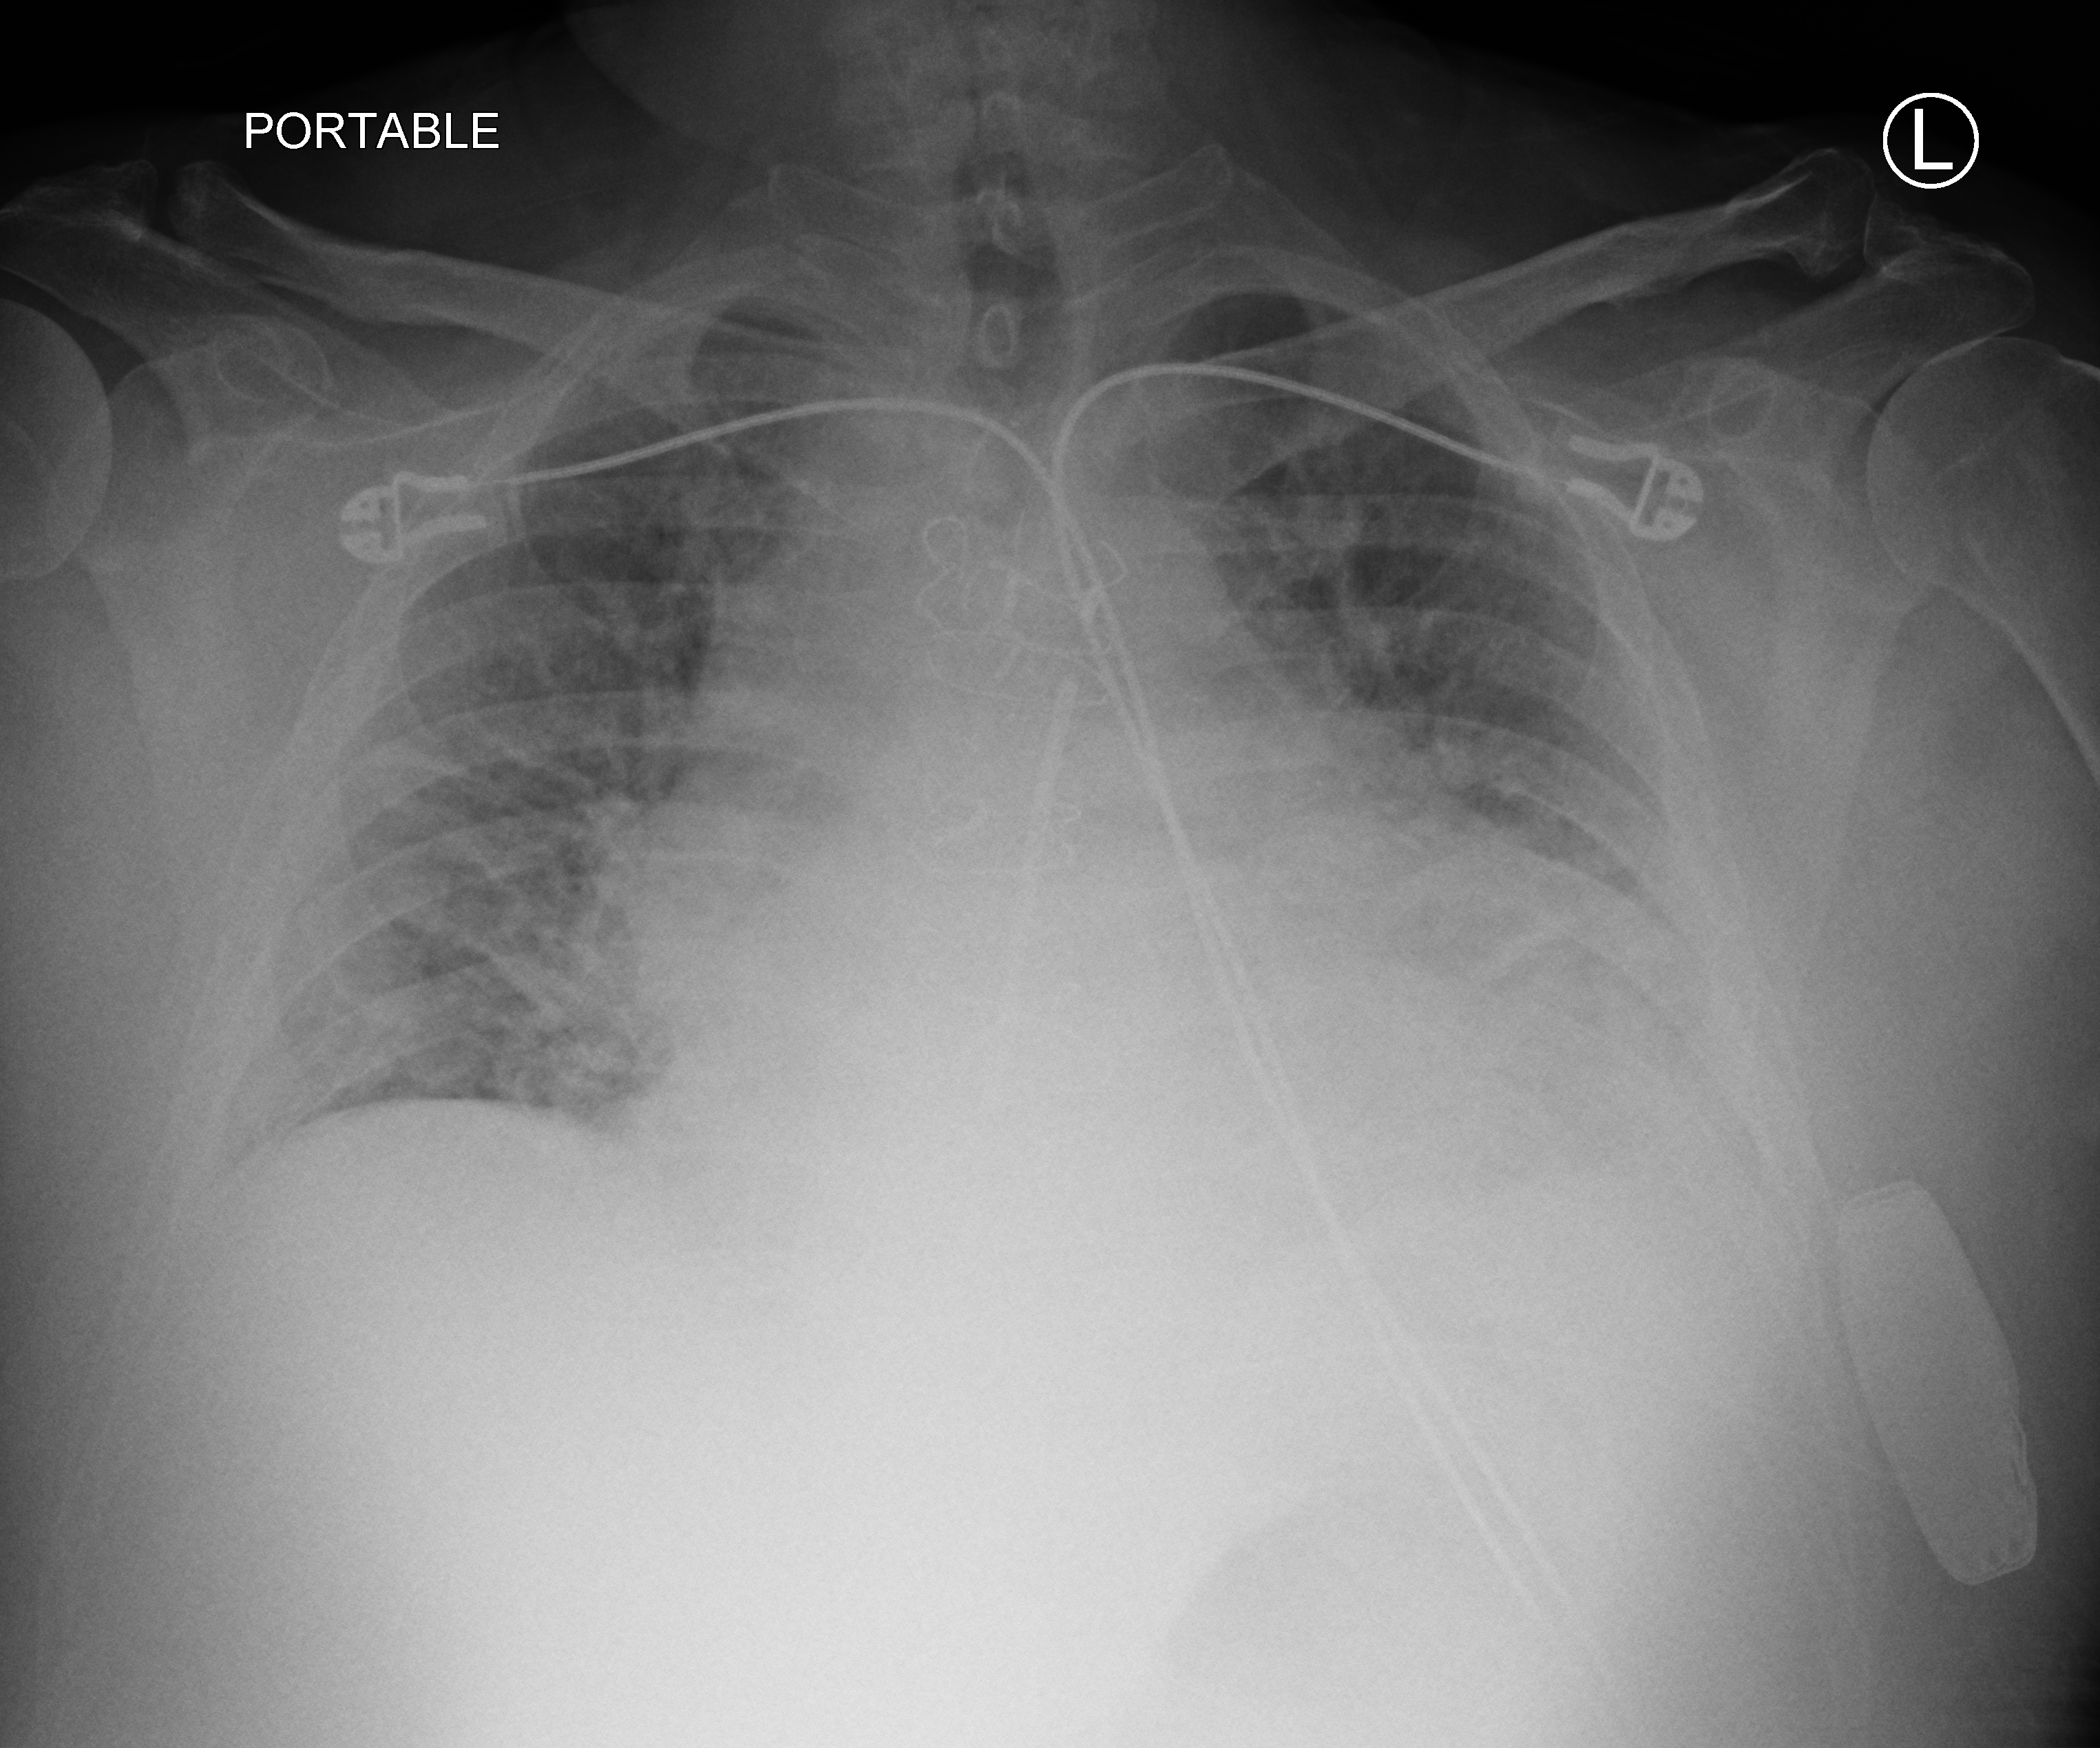
Chest X-ray (portable), anteroposterior (AP) projection. Male patient hospitalised with COVID-19, age 60–74 years.
Hospital-stay facts (about this admission, not read from this image; timing relative to this image not recorded): mechanically ventilated during this hospital stay: no; admitted to intensive care during this hospital stay: no.